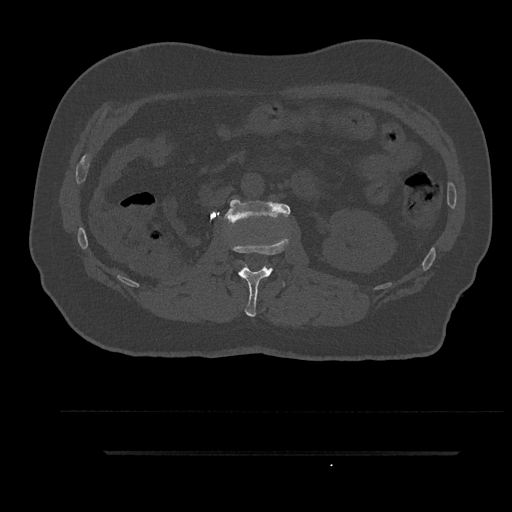
CT including the spine, one axial slice. 120 kVp. Bone window (W 1800 / L 400 HU). 0.5 mm slice thickness. 512 × 512 image matrix, field of view 432 × 432 mm. Male patient, age 63 years. Case-level facts recorded for this patient, not image findings: primary cancer: renal; vertebrae with lytic lesions (as recorded): T8.
Annotated regions visible in this slice (semi-automatically segmented with operator editing):
- L1 vertebra: bounding box <231,237,289,317> (left, top, right, bottom; pixels)
- L2 vertebra: <224,199,291,224>